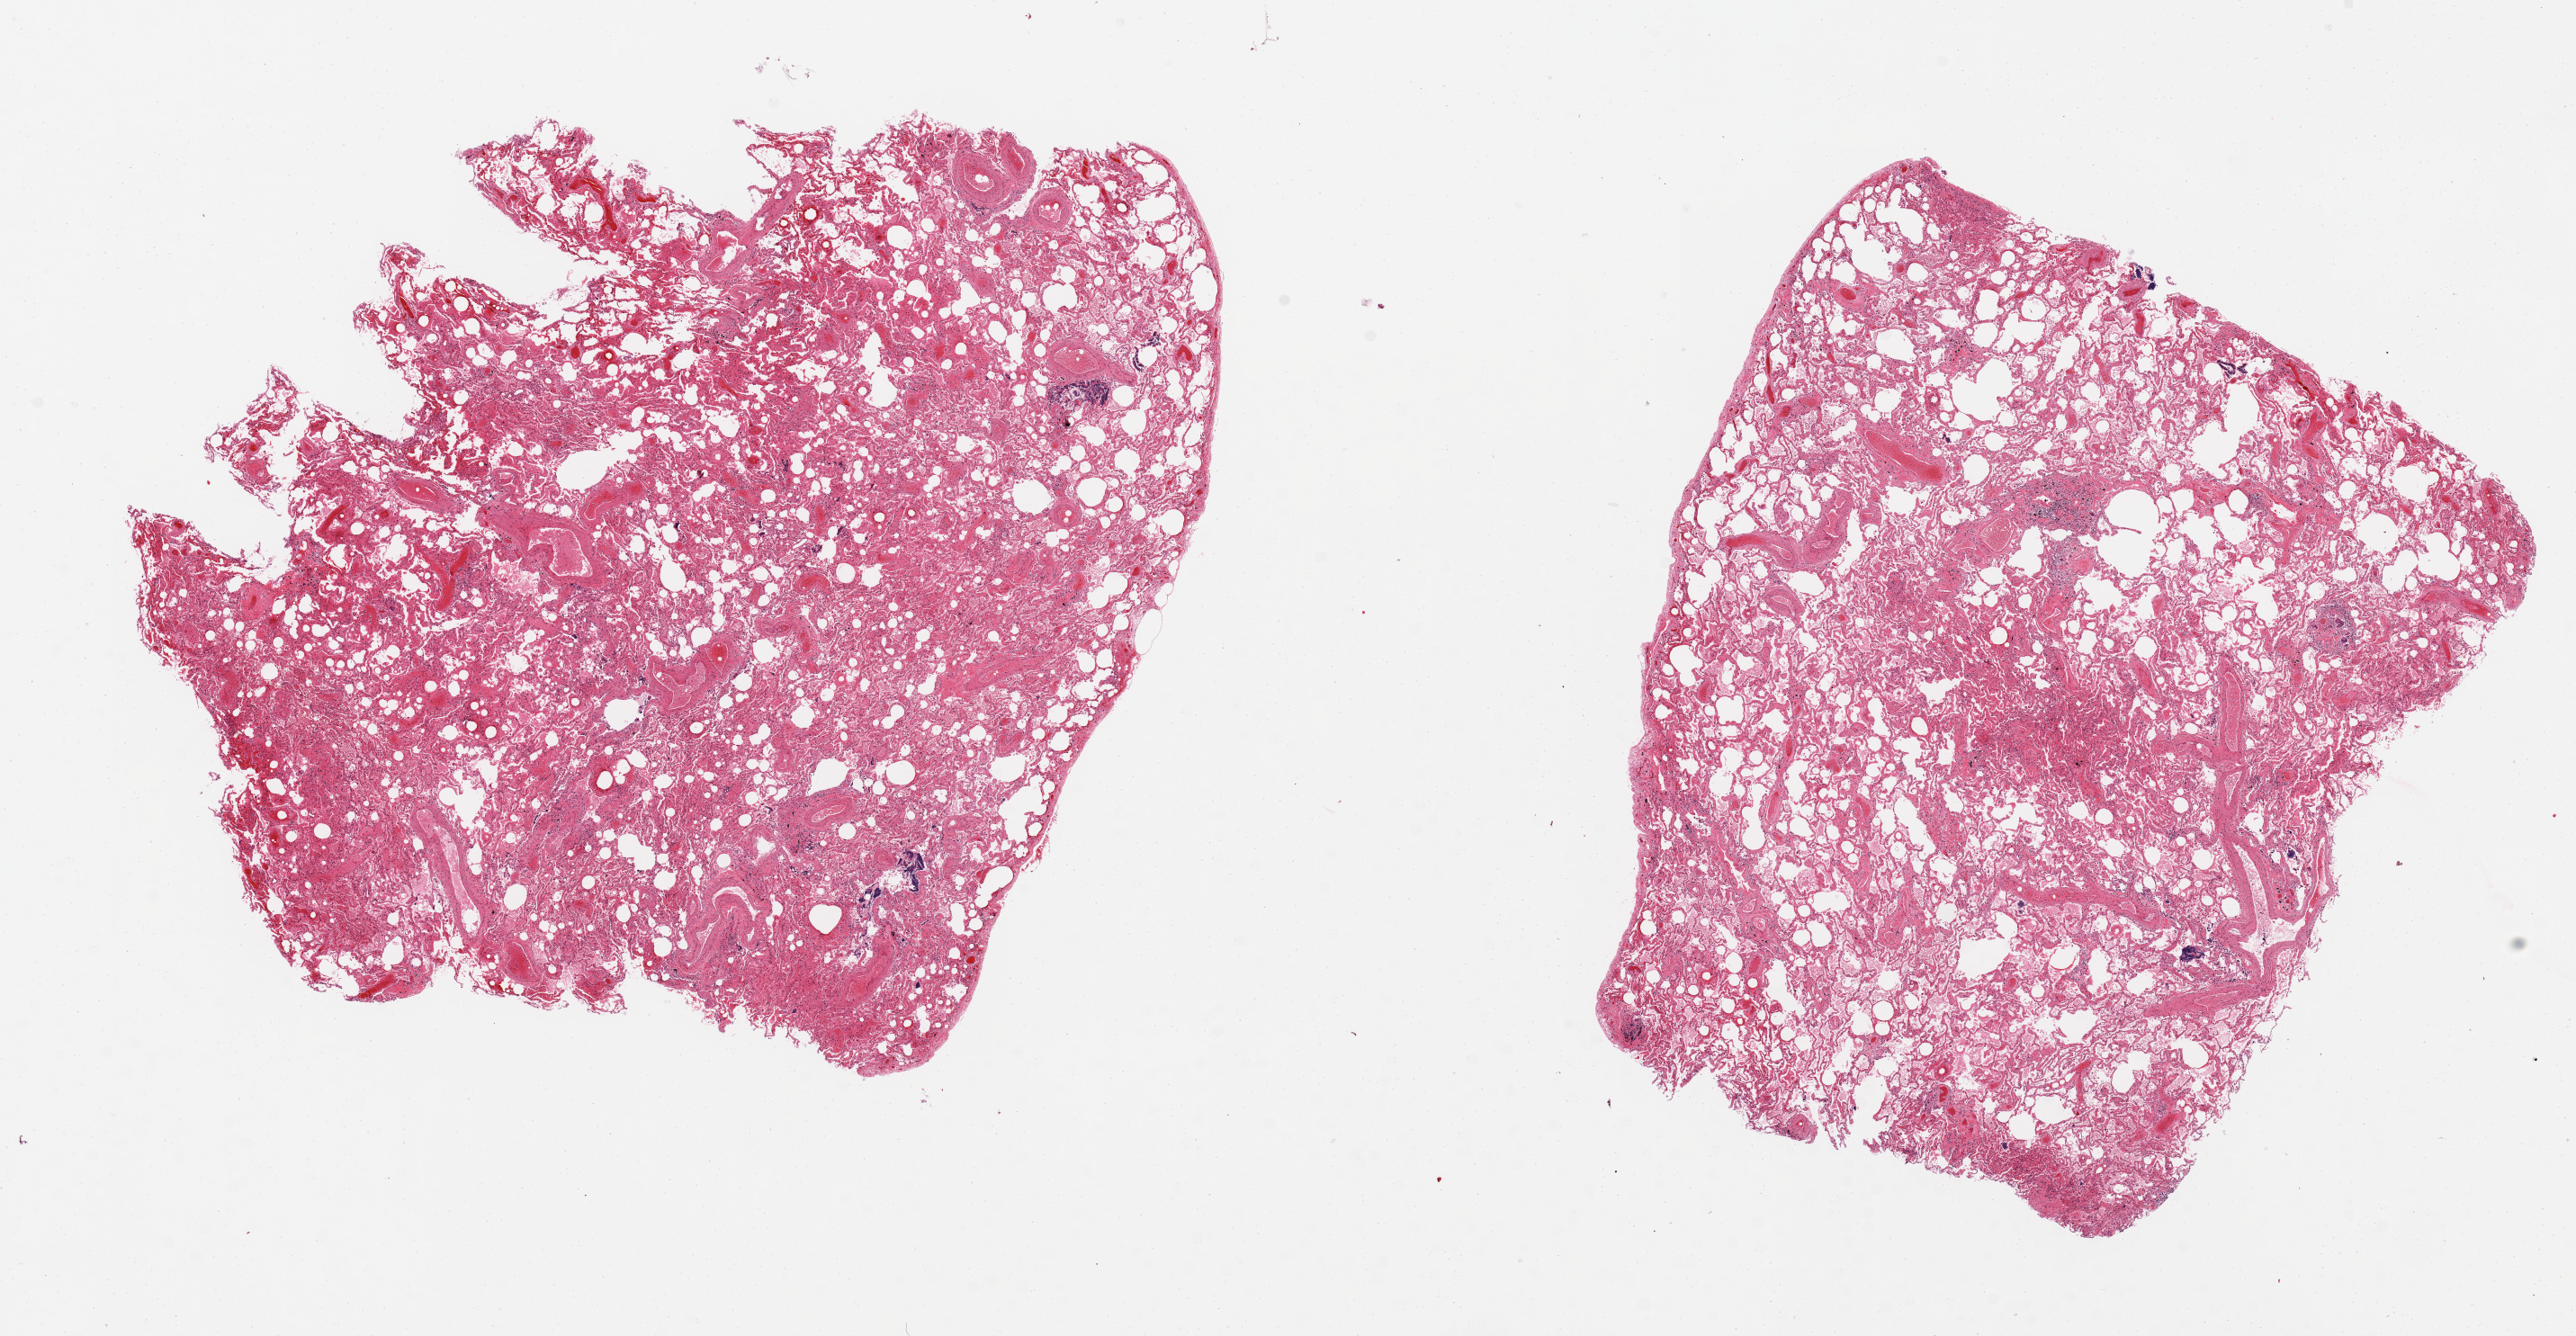
Whole-slide image, H&E stain, low-resolution overview of the scanned area, about 22.6 x 11.7 mm, PAXgene-fixed paraffin-embedded (PFPE) section, target tissue: lung, donor tissue sample. Donor: male.
Review note (as recorded): 2 pieces; chronic passive congestion with fibrosis, emphysema; foreign body giant cells consistent with aspiration.